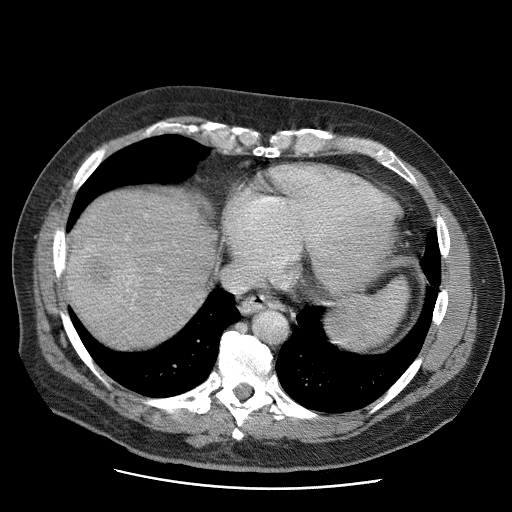
Contrast-enhanced abdominal CT (liver protocol), one axial slice. Position 56 of 81 along the scan axis. Reconstruction kernel STANDARD. 120 kVp. Soft-tissue window (W 400 / L 40 HU). 2.5 mm slice thickness. 512 × 512 image matrix. Case-level facts recorded for this patient, not image findings: diagnosis: hepatocellular carcinoma (patient treated with transarterial chemoembolisation; whether this scan precedes or follows treatment is not stated here); TNM stage (as recorded): Stage-IIIA; Child-Pugh class: A; tumour differentiation: moderately differentiated; tumour nodularity: multinodular.
Annotated regions visible in this slice (semi-automatic segmentation, software-assisted and operator-edited):
- liver parenchyma outside the tumour (the mass and vessels are separate outlines, so this box may not span the whole liver): box from (x=64, y=190) to (x=214, y=348) px
- mass: (x=65, y=232)–(x=139, y=321)